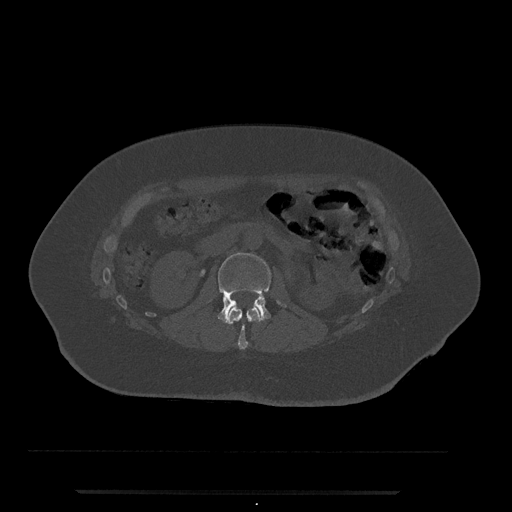
CT including the spine, one axial slice; slice 60 of 797 in the series (ordered by position); 120 kVp; bone window (W 1800 / L 400 HU); 0.5 mm slice thickness; 512 × 512 image matrix, field of view 440 × 440 mm. Female patient, age 51 years. From the clinical record (not read from this slice): primary cancer: neuro.
Structures marked on this image (semi-automatically segmented with operator editing):
- L1 vertebra: box from (x=225, y=307) to (x=261, y=350) px
- L2 vertebra: (x=218, y=253)–(x=285, y=323)